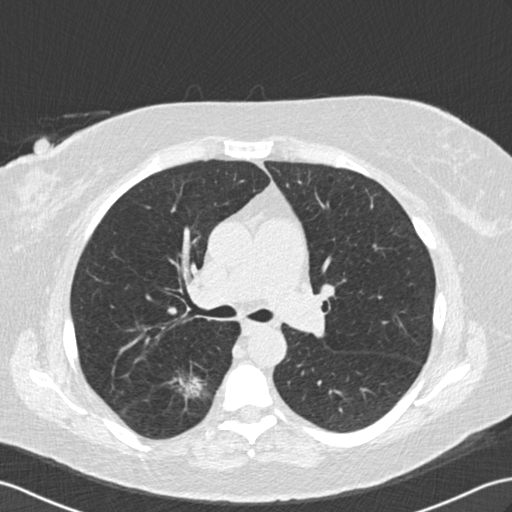
Axial slice from a low-dose chest CT screening exam; second screening round (one year after baseline); lung window (W 1500 / L -600 HU); slice 58 of 154 in the series; 512 × 512 image matrix, field of view 352 × 352 mm. Female participant, aged 65 years at enrolment. Former smoker at enrolment.
Lesion marked by an expert reader, bounding box [x1, y1, x2, y2] px = [157, 357, 215, 414]. Reader record for this screening exam (exam-level; its link to the box is not recorded): non-calcified nodule or mass ≥4 mm, right lower lobe, 18 × 16 mm, spiculated (stellate) margins, soft tissue attenuation, pre-existing on the prior screen: yes; interval growth: yes. Official screen result: positive, other. Participant outcome: lung cancer diagnosed 239 days after this screen — adenocarcinoma, NOS, right lower lobe, moderately differentiated (G2), stage IA (AJCC 6th edition), 25 mm at pathology.